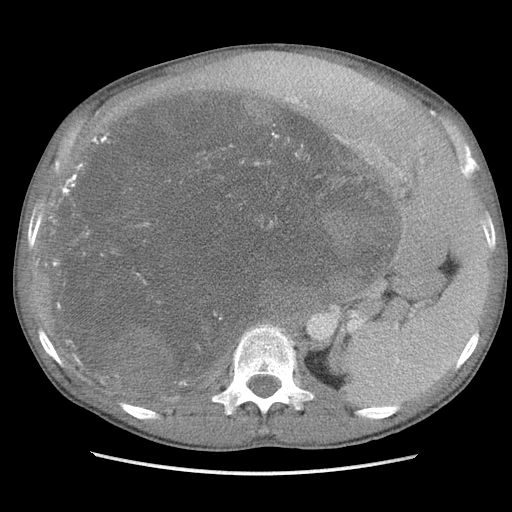
Contrast-enhanced abdominal CT, one axial slice. Position 70 of 115 along the scan axis. Soft-tissue window (W 400 / L 40 HU). 512 × 512 image matrix, field of view 360 × 360 mm. Male patient. Case-level facts recorded for this patient, not image findings: diagnosis: adrenocortical carcinoma; tumour side: right adrenal; Ki-67 index: 13 %; stage (as recorded): 3.
Annotated regions visible in this slice (semi-automatic segmentation, software-assisted and operator-edited):
- mass: bounding box [x1, y1, x2, y2] px = [55, 90, 394, 390]